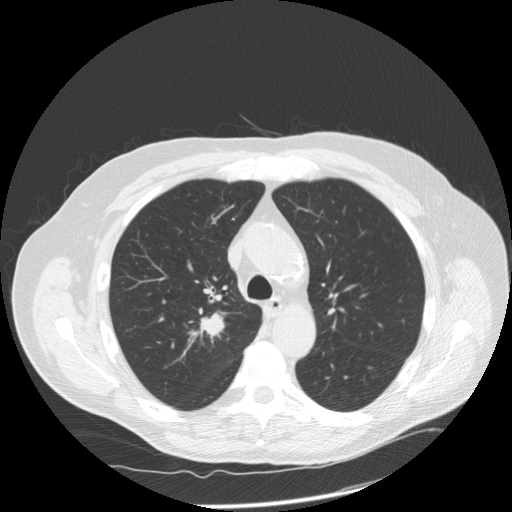
Low-dose screening chest CT, axial slice, third screening round (two years after baseline), lung window (W 1500 / L -600 HU), standard (soft-tissue) reconstruction kernel (STANDARD), slice 51 of 166 in the series, 512 × 512 image matrix, field of view 390 × 390 mm. Male participant, aged 69 years at enrolment. Former smoker at enrolment.
Lesion marked by an expert reader, box from (x=183, y=301) to (x=242, y=350) px. Reader record for this screening exam (exam-level; its link to the box is not recorded): non-calcified nodule or mass ≥4 mm, right upper lobe, 18 × 17 mm, spiculated (stellate) margins, soft tissue attenuation, pre-existing on the prior screen: no. Later outcome: lung cancer diagnosed 13 days after this screen — squamous cell carcinoma, NOS, right upper lobe, poorly differentiated (G3), stage IA (AJCC 6th edition), 22 mm at pathology.